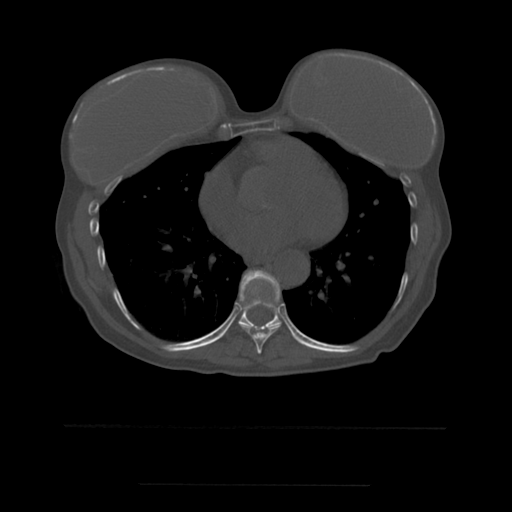
CT including the spine, one axial slice; position 331 of 544 along the scan axis; bone window (W 1800 / L 400 HU); 1.25 mm slice thickness; 512 × 512 image matrix, field of view 350 × 350 mm. Patient age 58 years. From the clinical record (not read from this slice): primary cancer: lung.
Annotated regions visible in this slice (semi-automatically segmented with operator editing):
- T8 vertebra: bounding box (x1, y1, x2, y2) in pixels: (238, 270, 282, 354)
- T9 vertebra: (216, 301, 282, 341)